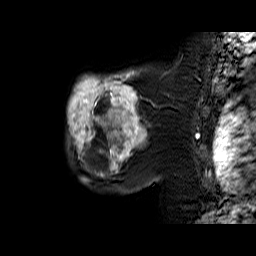
Breast MRI (dynamic contrast-enhanced), one sagittal slice. Slice 48 of 60 in the series (ordered by position). Dynamic contrast-enhanced series, time point 2 of 6 at this slice position (early post-contrast). 1.5 T. TE 6.4 ms, TR 32.9 ms. 4 mm slice thickness. 256 × 256 image matrix, field of view 200 × 200 mm. Female patient. Case-level facts recorded for this patient, not image findings: setting: breast cancer imaged before/during neoadjuvant chemotherapy; receptor status: triple-negative.
Annotated regions visible in this slice (semi-automatic segmentation, software-assisted and operator-edited):
- analysis volume of interest (the breast-tissue region the enhancement analysis was run in; not a lesion): box from (x=67, y=67) to (x=159, y=174) px
- tumour enhancement mask (voxels above the 100 % enhancement threshold inside the analysis volume of interest): (x=68, y=70)–(x=146, y=174)